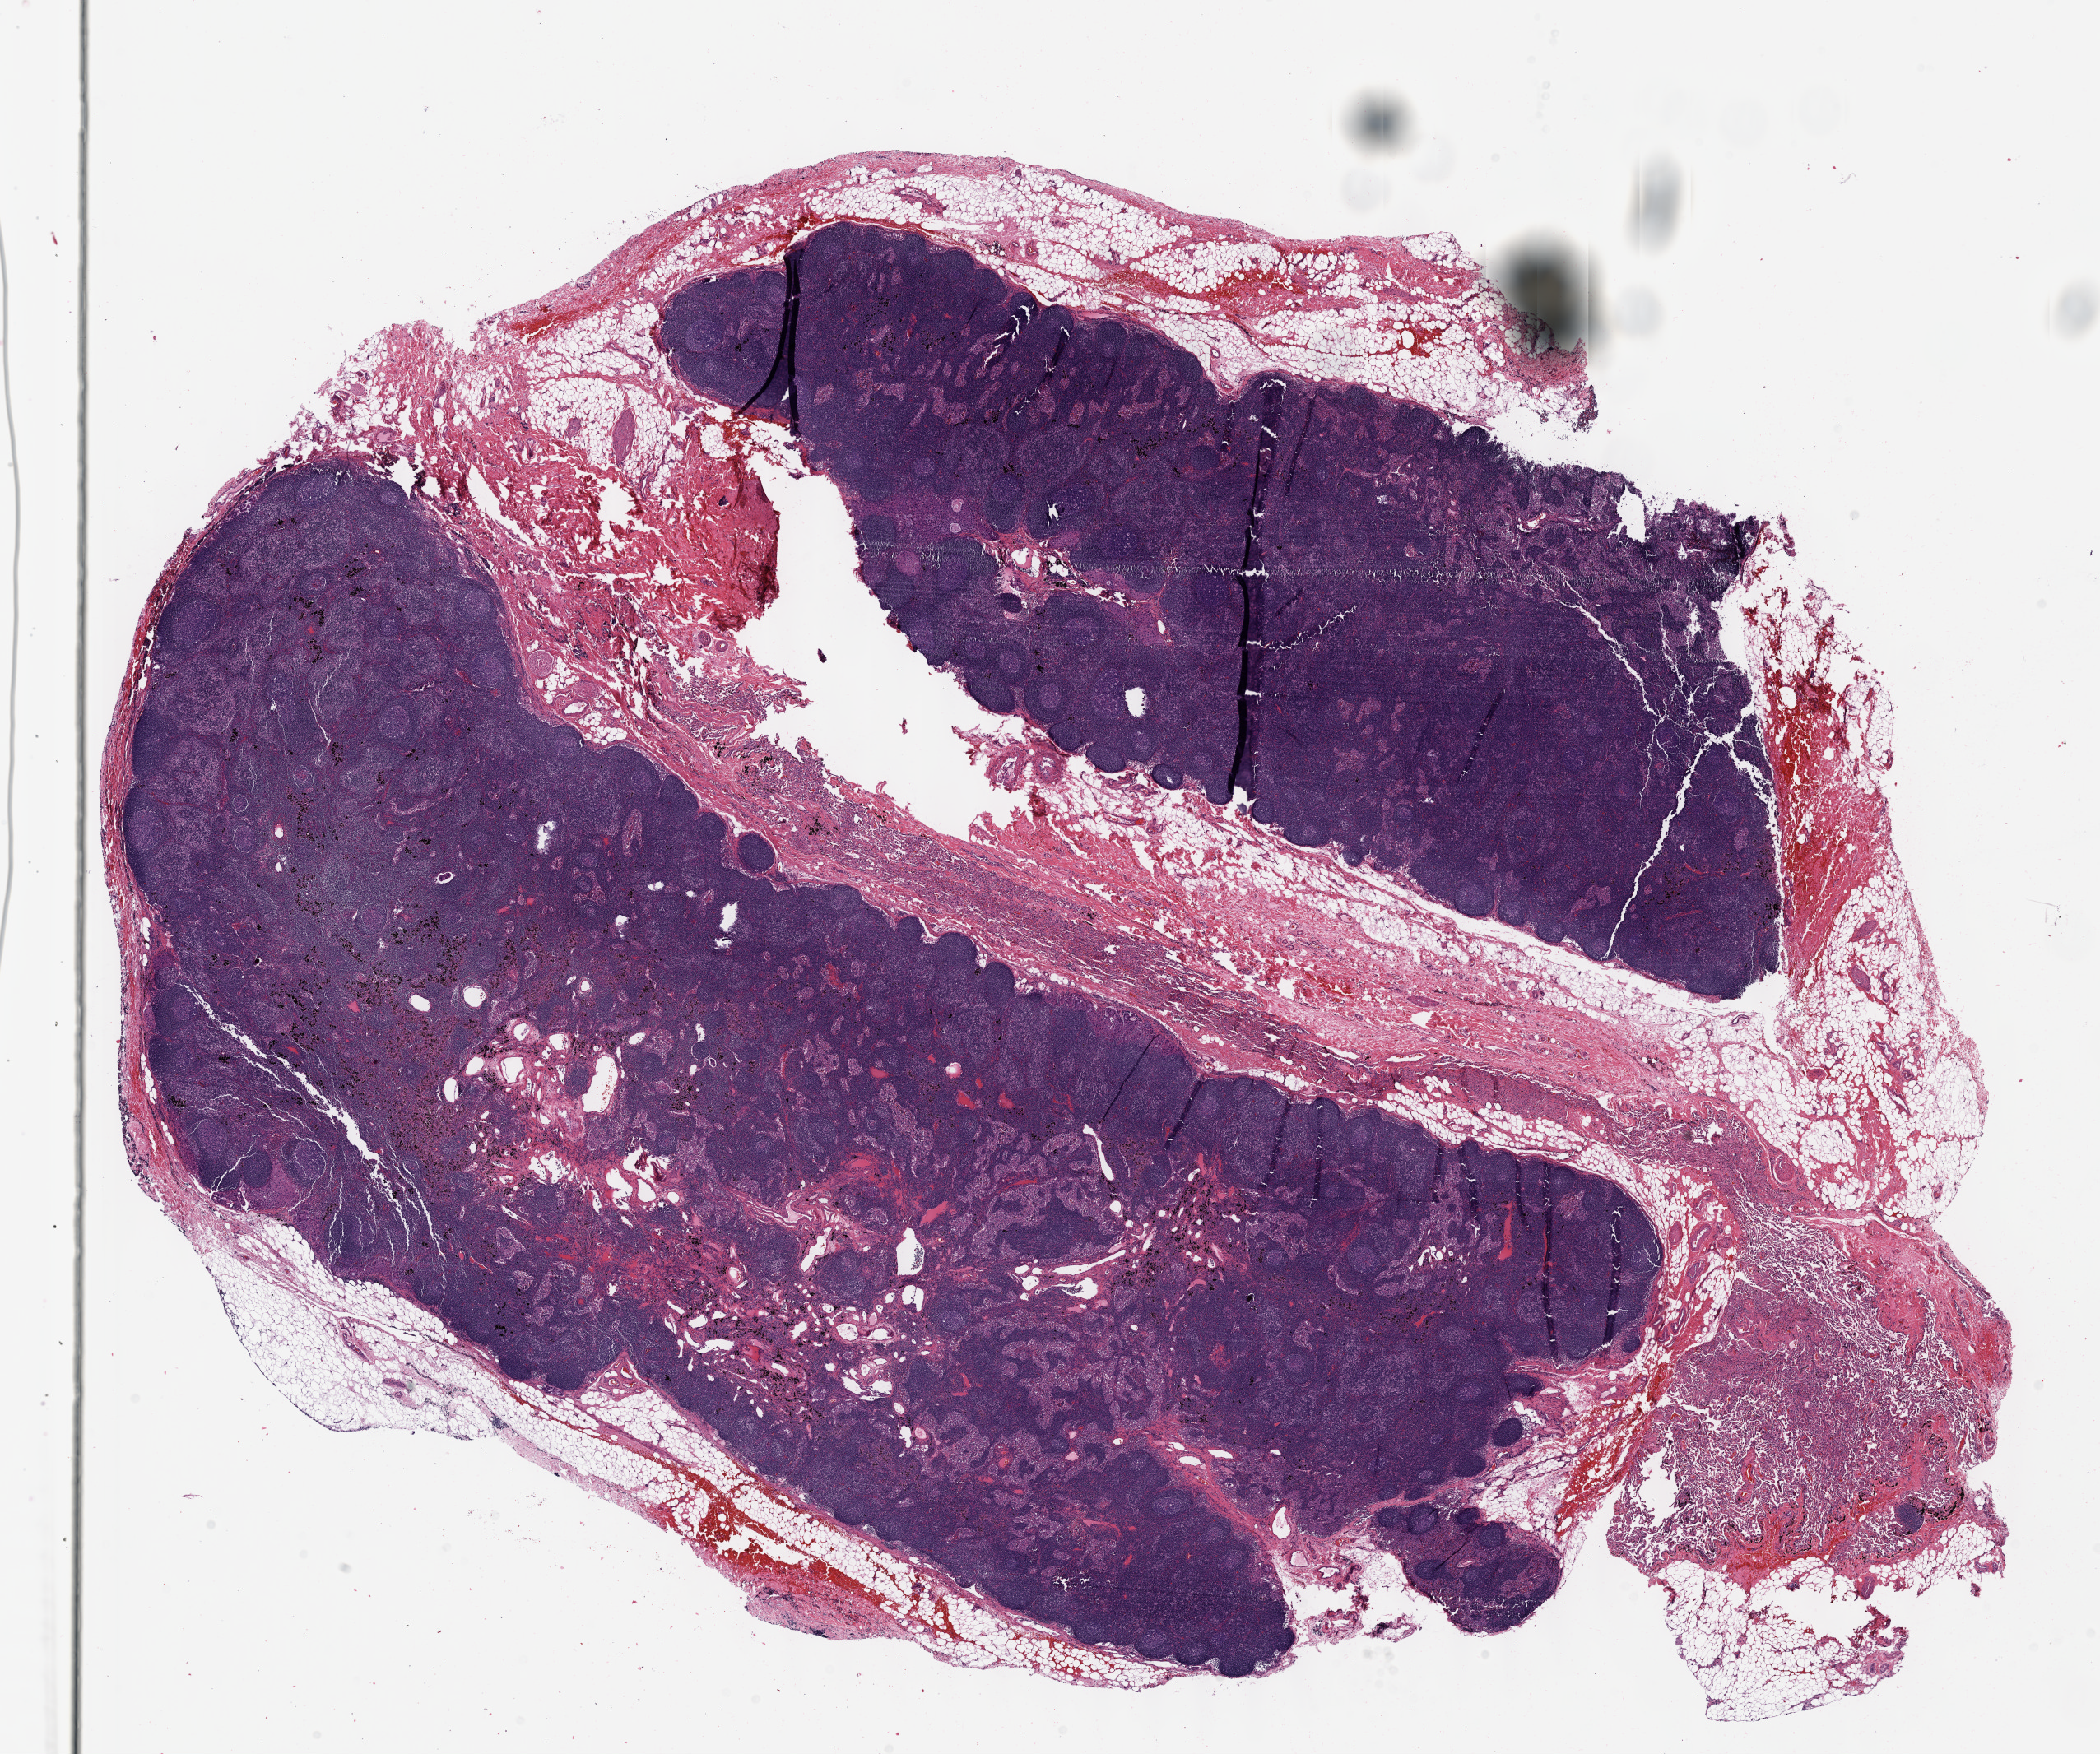
Digitized Hematoxylin and eosin (H&E) stained tissue section (whole slide) — whole scanned area (about 20.6 x 17.2 mm, from a 40x scan) shown as a low-resolution overview. Formalin-fixed paraffin-embedded (FFPE) diagnostic section. Lung, primary tumour sample. Male patient; age at initial diagnosis 49 years.
Laterality: left. AJCC pathologic stage: IIIA (7th edition). Histologic diagnosis: Adenocarcinoma, NOS (upper lobe, lung).